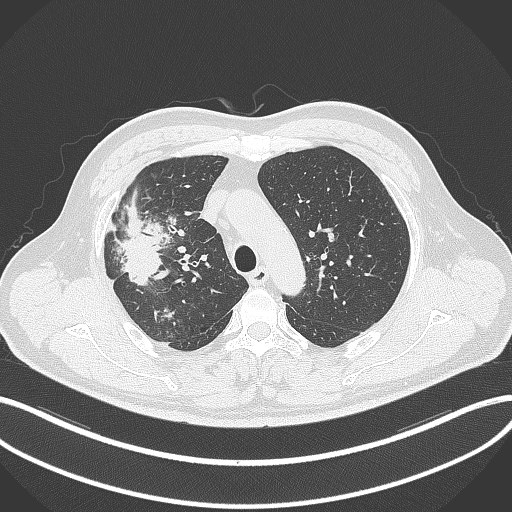
Chest CT, one axial slice; slice 251 of 348 in the series (ordered by position); reconstruction kernel B70f; lung window (W 1500 / L -600 HU); 512 × 512 image matrix. Patient: male, 55 years. From the clinical record (not read from this slice): clinical TNM (as recorded): T3 N2 M1.
Annotated regions visible in this slice (bounding box drawn by a radiologist):
- lung tumour (recorded histology: adenocarcinoma): bounding box (x1, y1, x2, y2) in pixels: (115, 201, 170, 286)